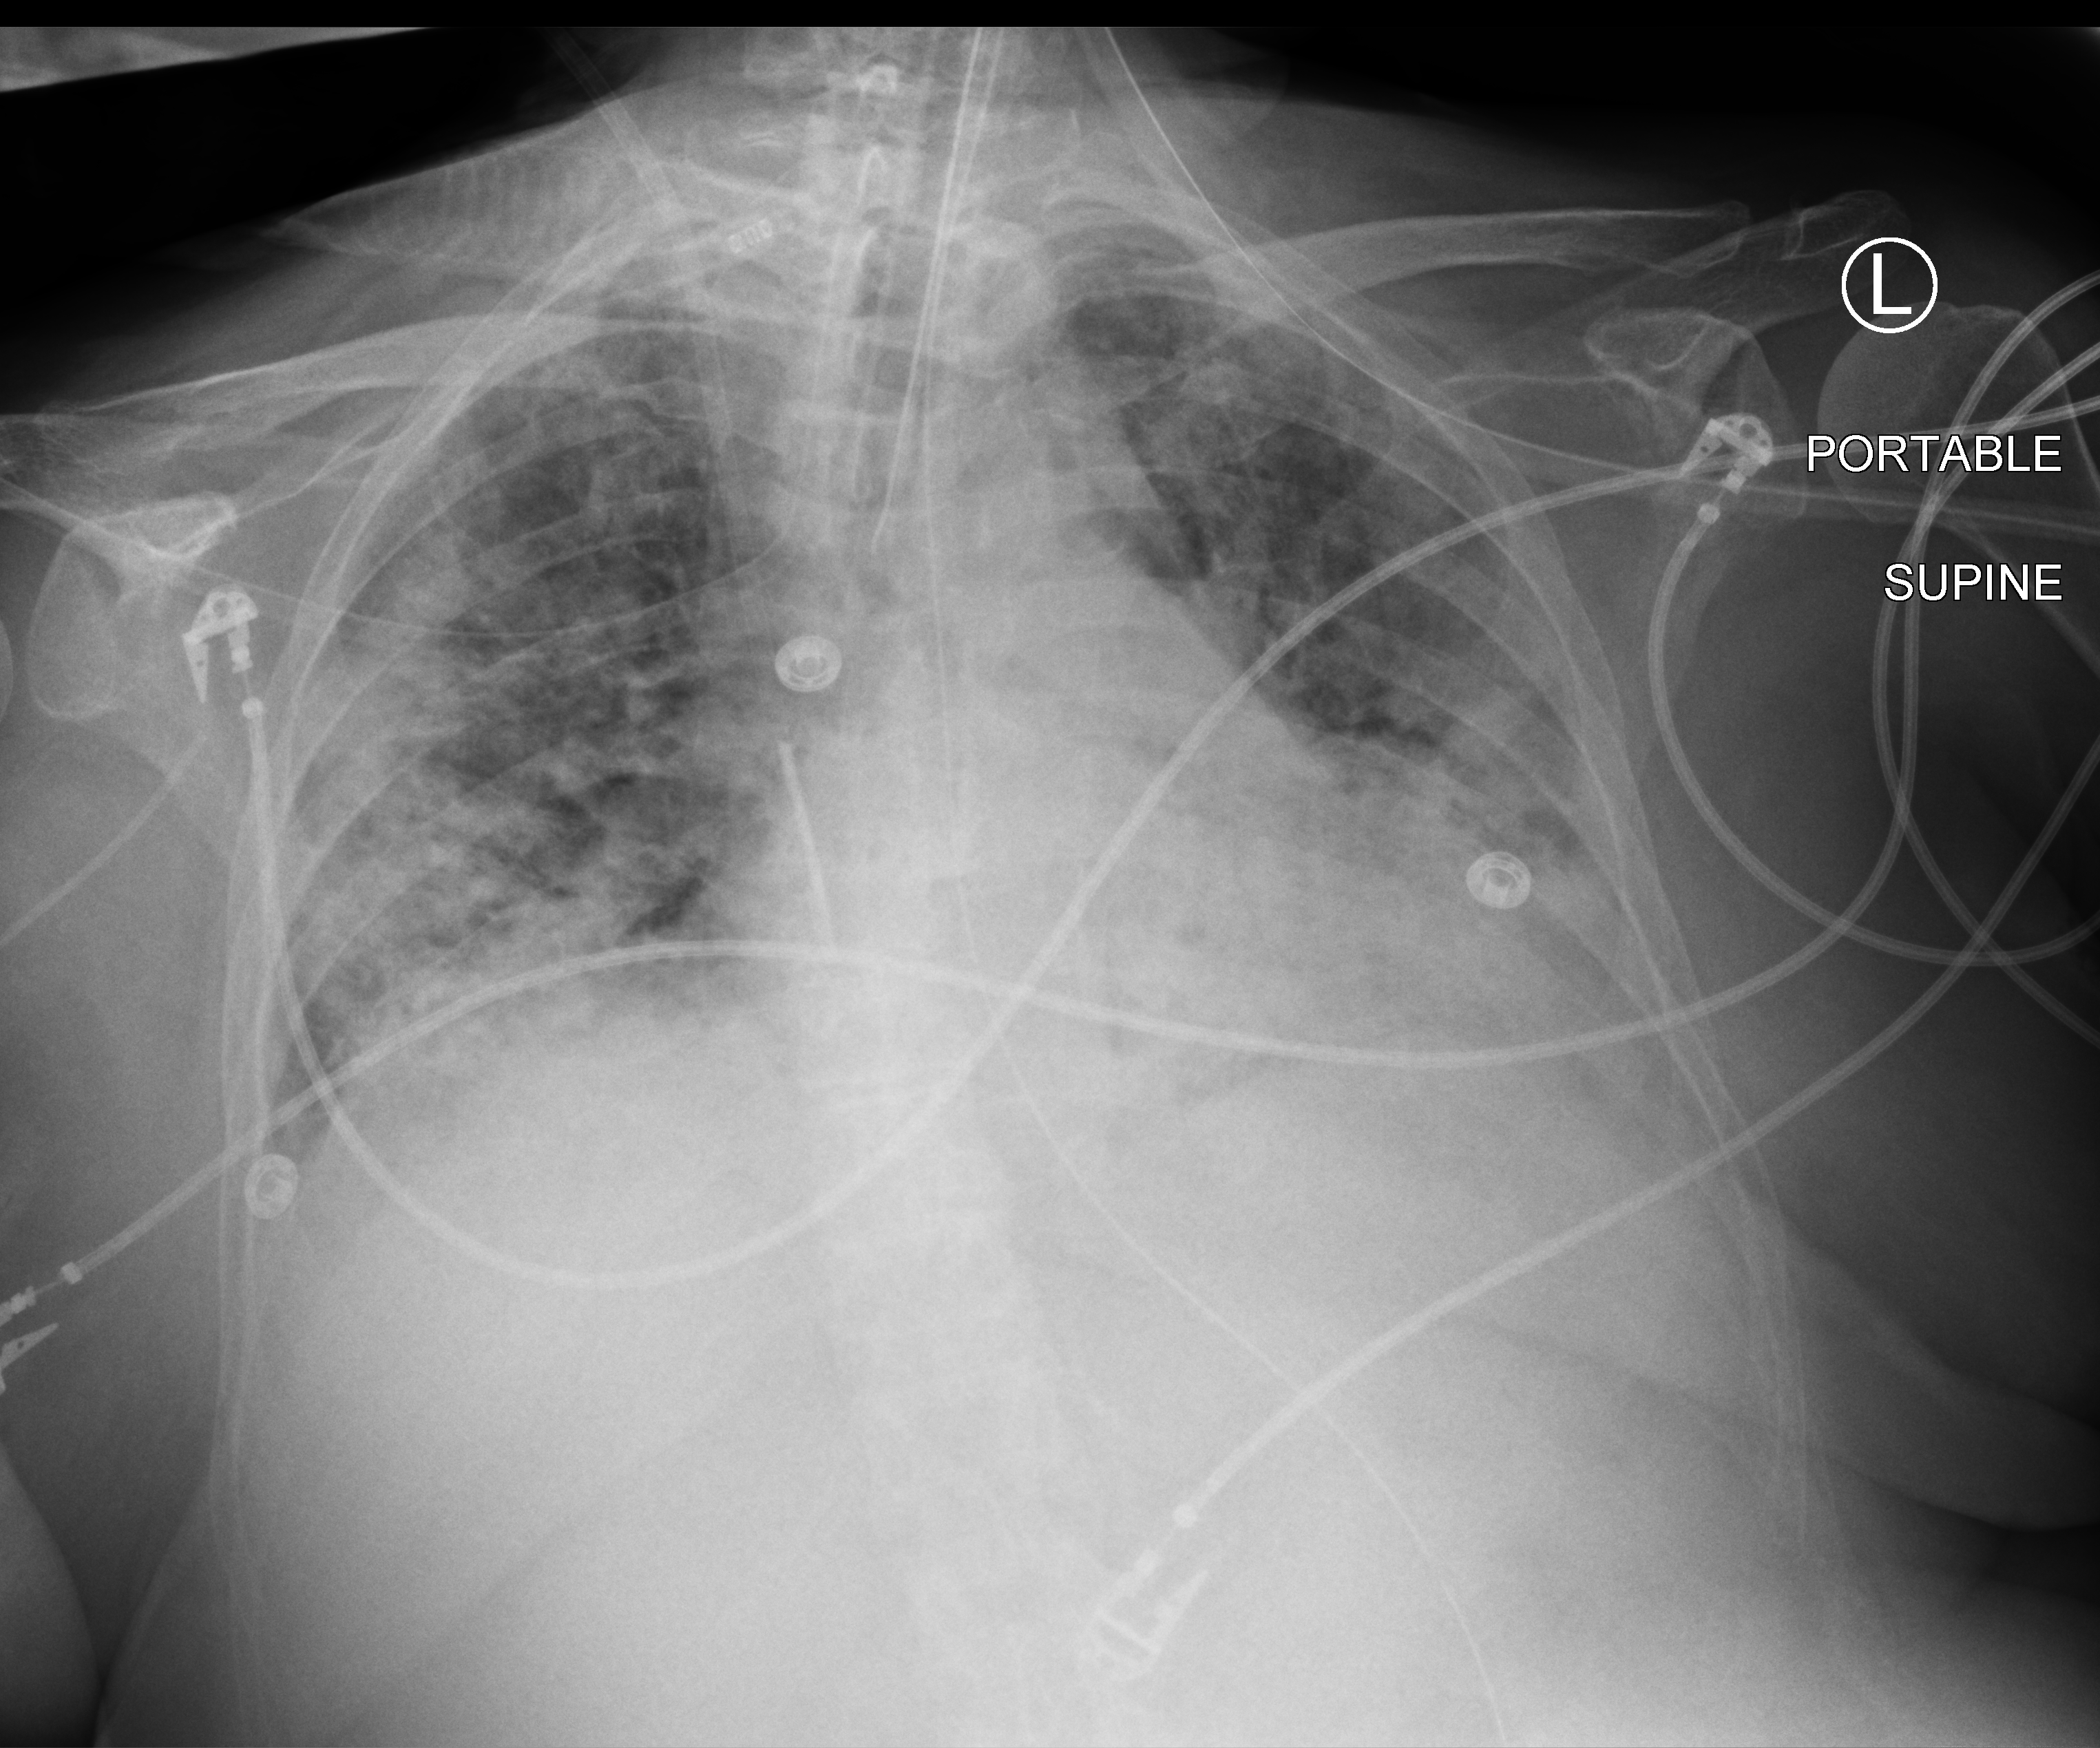
Portable chest radiograph, anteroposterior (AP) projection. Female patient hospitalised with COVID-19, age 75–90 years.
Admission-level facts for this patient (not findings on this image; timing relative to this image not recorded):
- admitted to intensive care during this hospital stay: yes